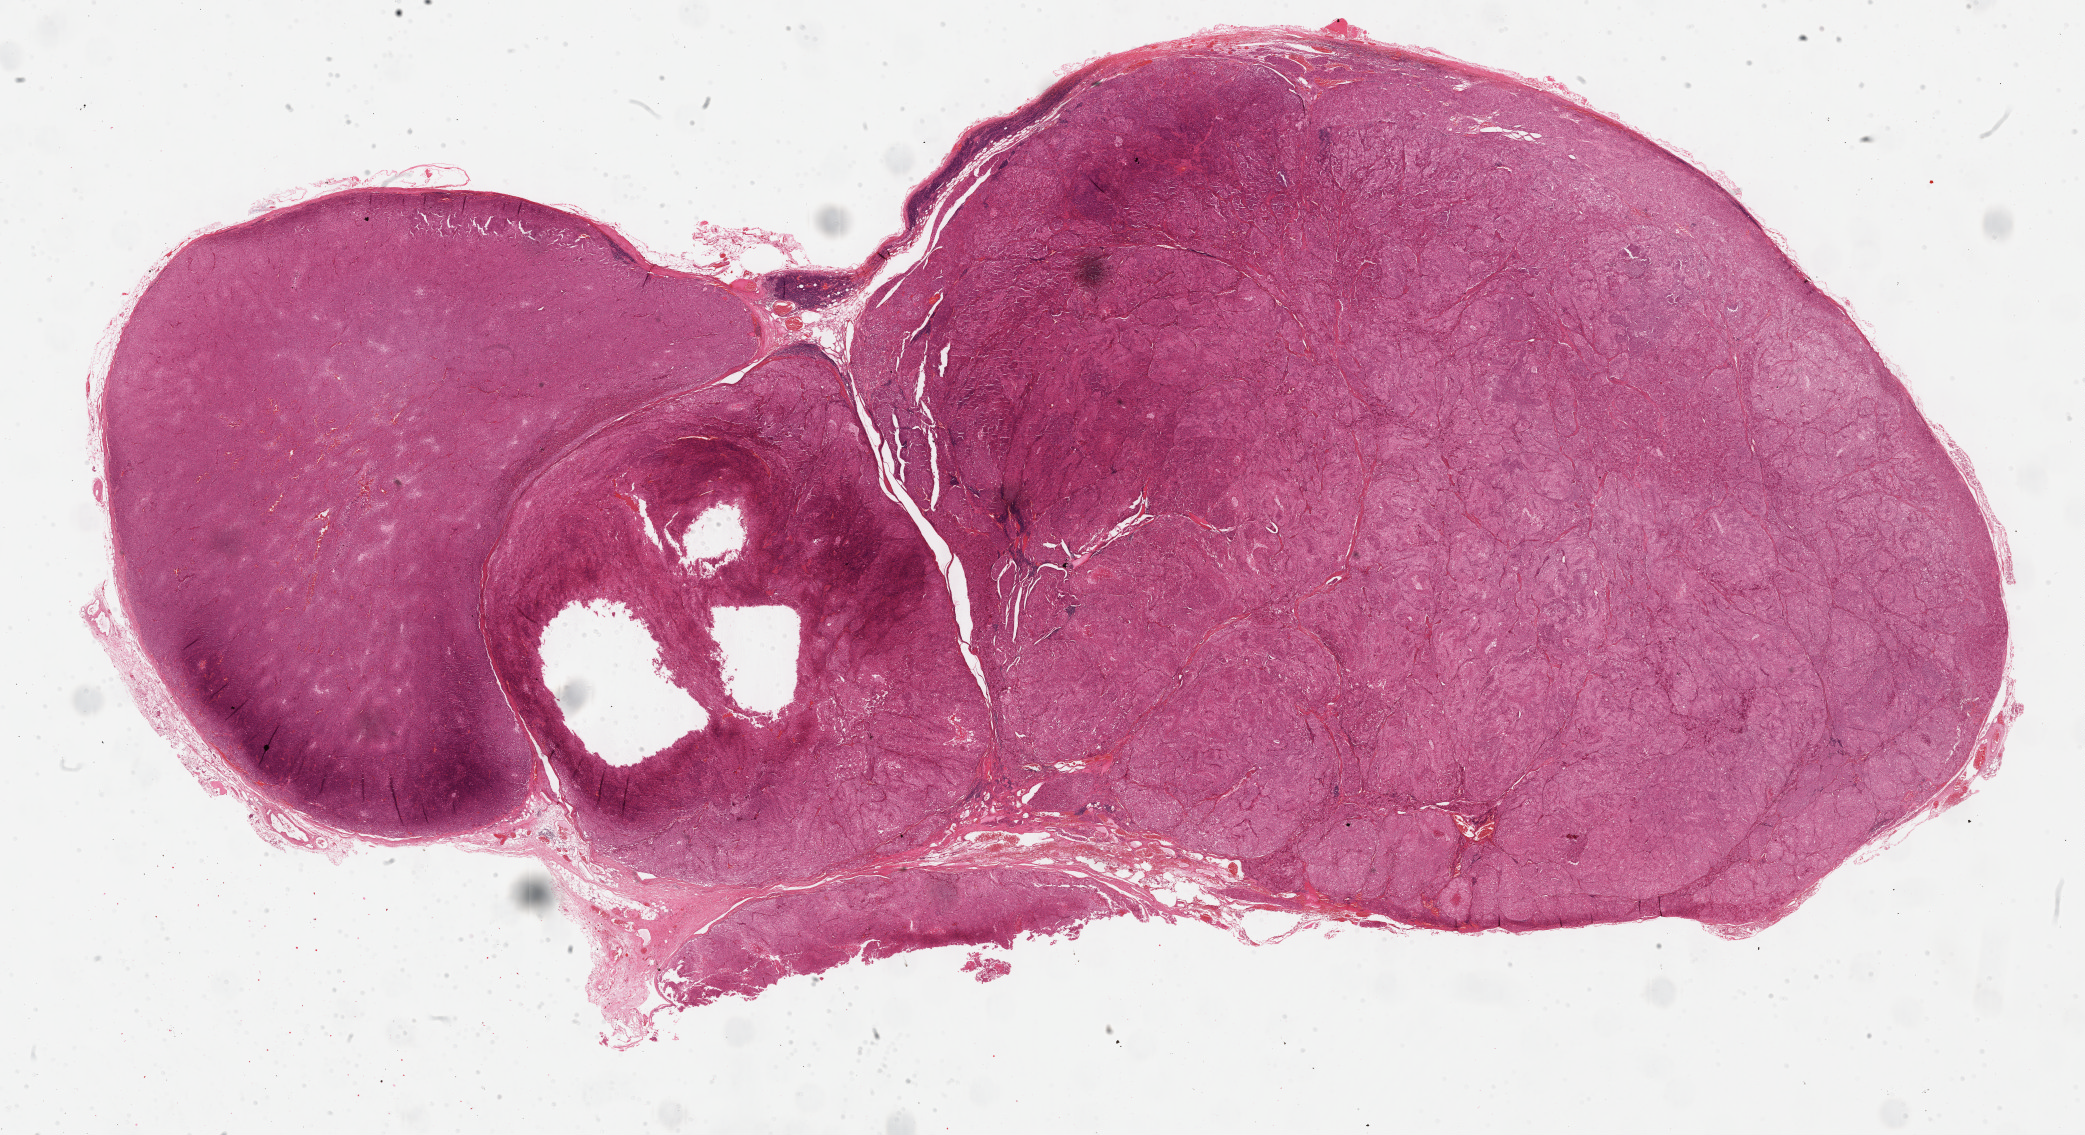
Whole-slide histology image, H&E-stained — low-resolution overview of the scanned area, about 33.7 x 18.4 mm, formalin-fixed paraffin-embedded (FFPE) diagnostic section, primary tumour sample from the adrenal cortex. Male patient; age at initial diagnosis 65 years.
* histologic diagnosis: Adrenal cortical carcinoma (cortex of adrenal gland)
* lymph nodes positive (case pathology): 6 of 6 examined
* laterality: left